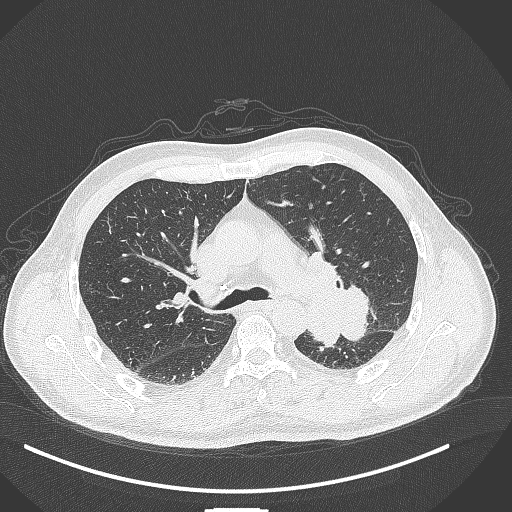
Chest CT, one axial slice; position 272 of 429 along the scan axis; lung window (W 1500 / L -600 HU); 1 mm slice thickness; 512 × 512 image matrix. Male patient, age 55 years. From the clinical record (not read from this slice): clinical TNM (as recorded): T3 N0 M1c; histopathological grade: G3.
Outlined on this slice (bounding box drawn by a radiologist):
- lung tumour (recorded histology: adenocarcinoma): box from (x=308, y=275) to (x=373, y=355) px